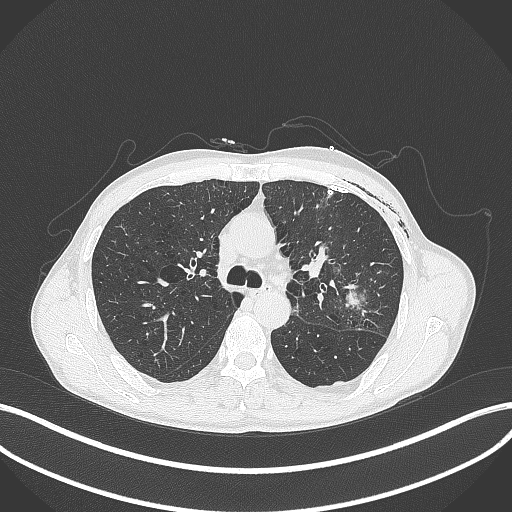
Chest CT, one axial slice. Slice 266 of 457 in the series (ordered by position). Reconstruction kernel B70f. 120 kVp. Lung window (W 1500 / L -600 HU). 1 mm slice thickness. 512 × 512 image matrix. Patient: male, 58 years. From the clinical record (not read from this slice): clinical TNM (as recorded): T3 N0 M0.
Outlined on this slice (rectangle marked by the reading radiologist):
- lung tumour (recorded histology: adenocarcinoma): bounding box [x1, y1, x2, y2] px = [341, 275, 366, 311]